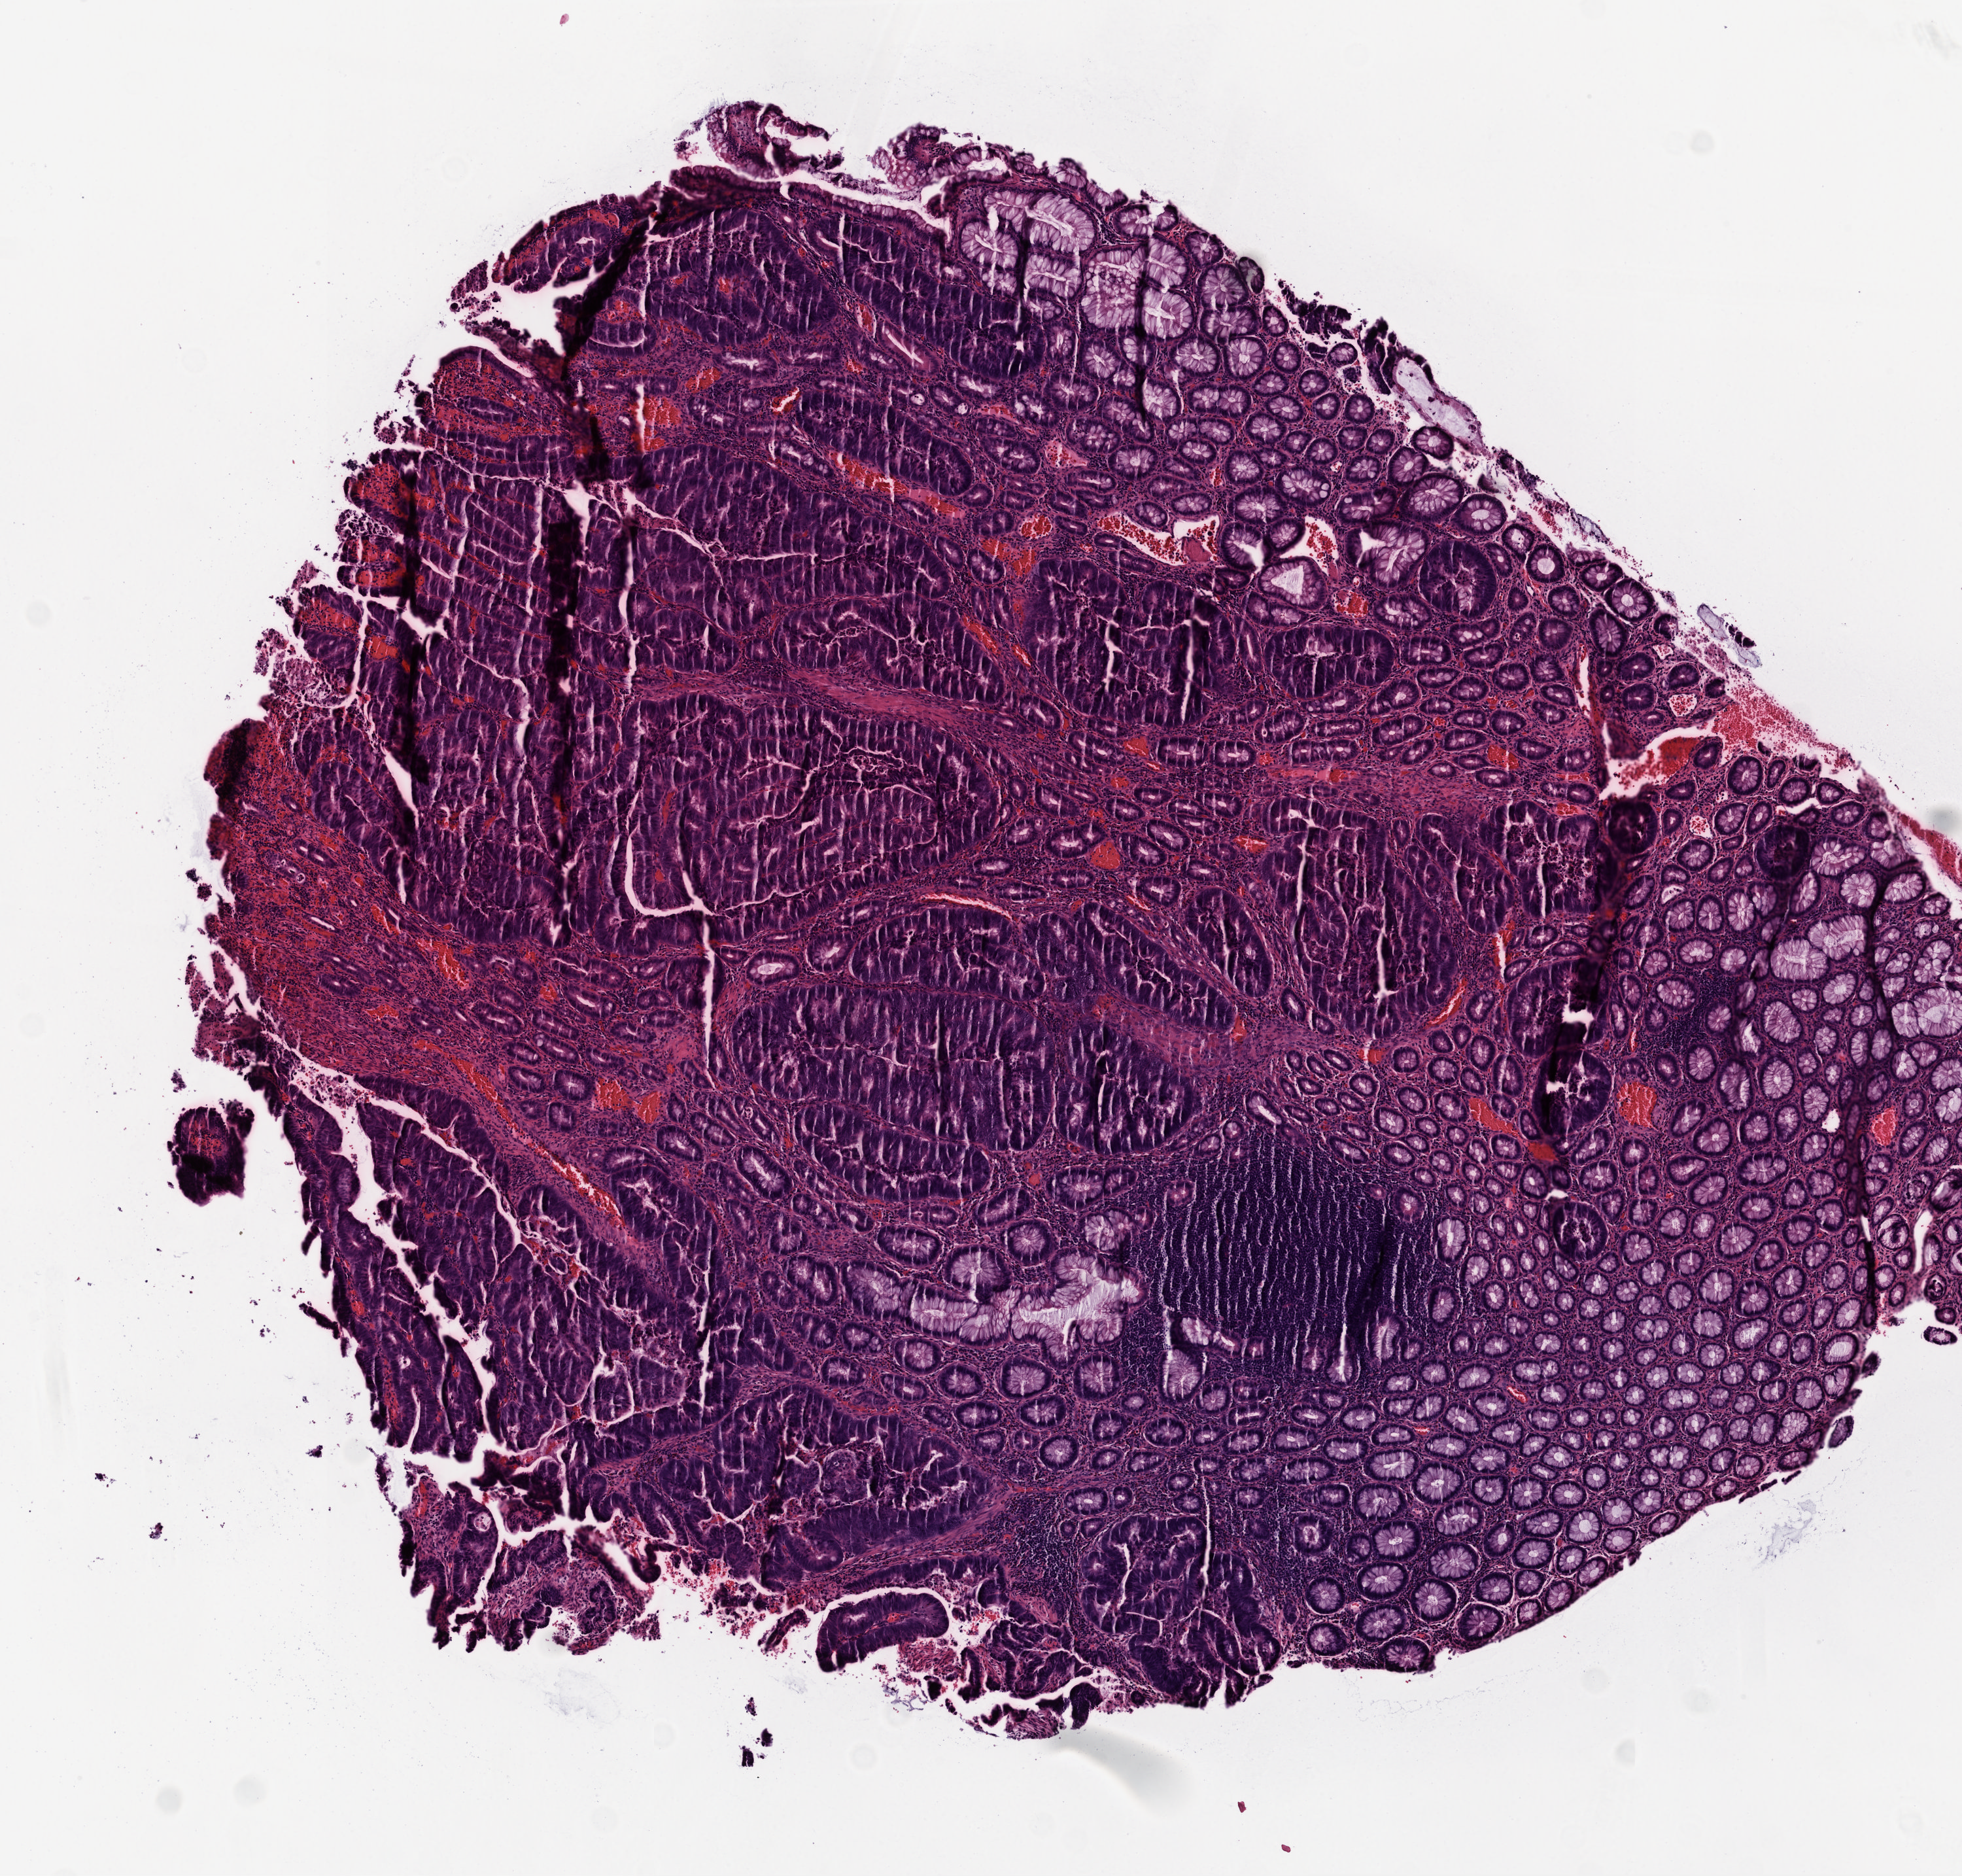
H&E-stained whole-slide image, whole scanned area (about 6.0 x 5.8 mm) shown as a low-resolution overview, frozen section from the top of the tissue portion, sample: primary tumour, rectum. Patient: female, age at initial diagnosis 54 years.
Diagnosis: Adenocarcinoma, NOS.